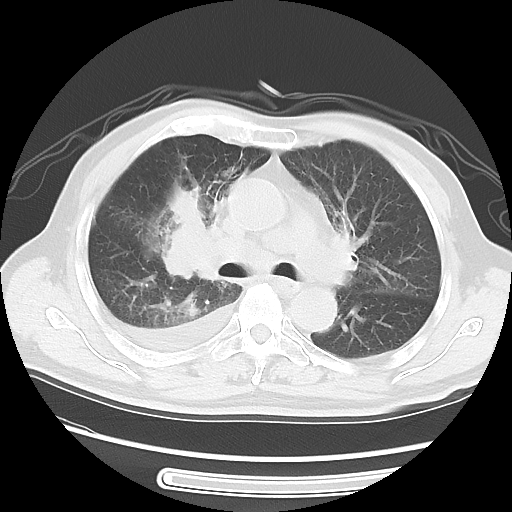
Chest CT, one axial slice; reconstruction kernel LUNG; lung window (W 1500 / L -600 HU); 5 mm slice thickness; 512 × 512 image matrix, field of view 360 × 360 mm. Male patient, age 77 years. From the clinical record (not read from this slice): clinical TNM (as recorded): T3 N3 M1b.
Structures marked on this image (rectangle marked by the reading radiologist):
- lung tumour (recorded histology: small cell carcinoma): bounding box (x1, y1, x2, y2) in pixels: (151, 171, 225, 291)